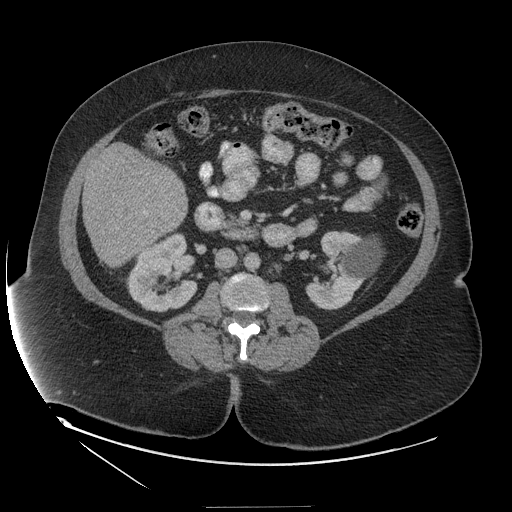
Contrast-enhanced abdominal CT (liver protocol), one axial slice; position 44 of 127 along the scan axis; reconstruction kernel STANDARD; soft-tissue window (W 400 / L 40 HU); 2.5 mm slice thickness; 512 × 512 image matrix, field of view 480 × 480 mm. From the clinical record (not read from this slice): diagnosis: hepatocellular carcinoma (patient treated with transarterial chemoembolisation; whether this scan precedes or follows treatment is not stated here); TNM stage (as recorded): Stage-II; Child-Pugh class: A; tumour nodularity: multinodular; tumour size: 3 cm.
Outlined on this slice (semi-automatically segmented with operator editing):
- liver parenchyma outside the tumour (the mass and vessels are separate outlines, so this box may not span the whole liver): bounding box (x1, y1, x2, y2) in pixels: (82, 144, 188, 266)